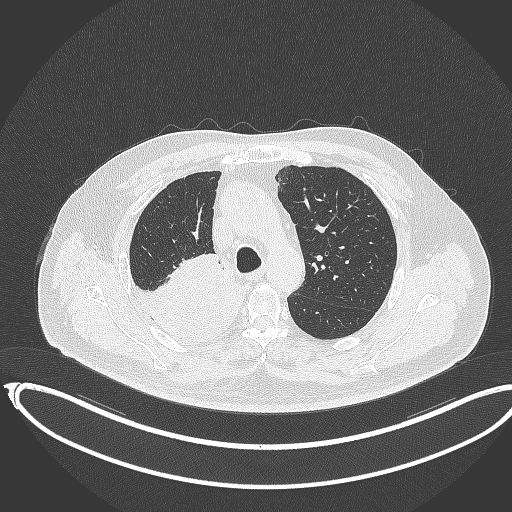
Chest CT, one axial slice; slice 259 of 403 in the series (ordered by position); reconstruction kernel B70f; lung window (W 1500 / L -600 HU); 1 mm slice thickness; 512 × 512 image matrix. Patient: male, 68 years. Case-level facts recorded for this patient, not image findings: clinical TNM (as recorded): T2a N0 M0.
Annotated regions visible in this slice (rectangle marked by the reading radiologist):
- lung tumour (recorded histology: adenocarcinoma): bounding box <135,260,250,341> (left, top, right, bottom; pixels)